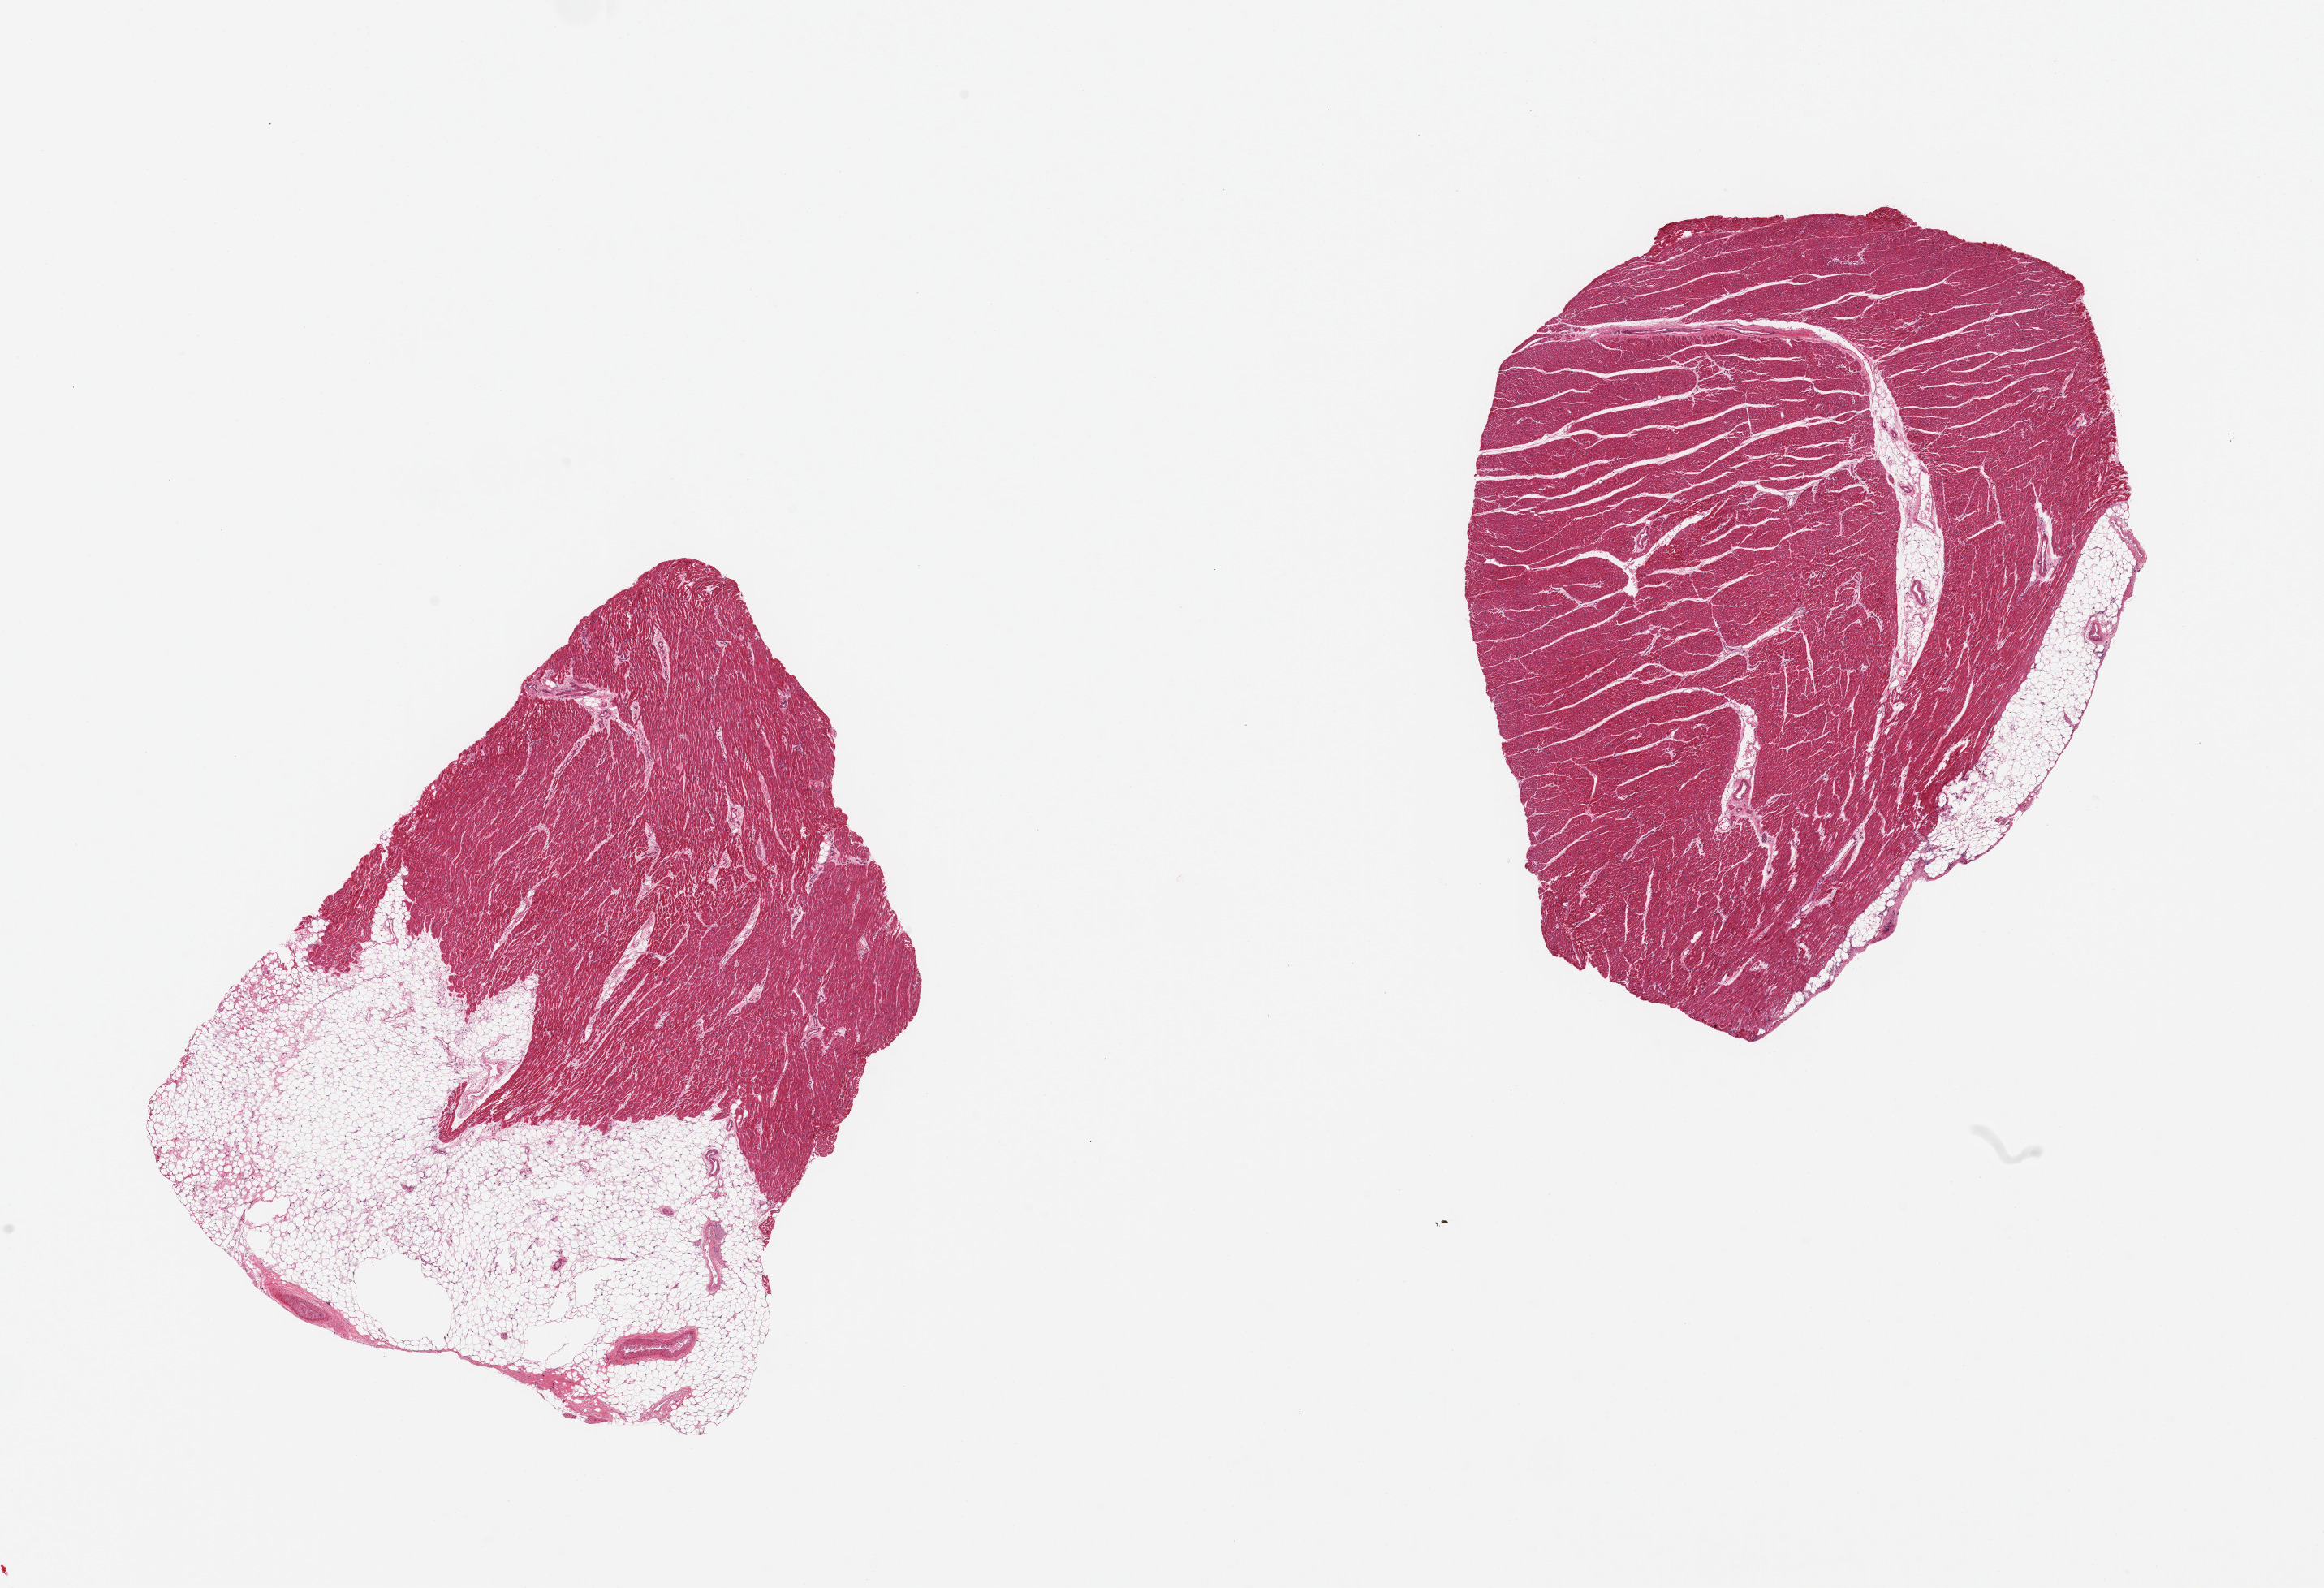
Digitized hematoxylin and eosin (H&E)-stained section, whole scanned area (about 22.6 x 15.5 mm, acquisition: 20x scan) shown as a low-resolution overview; PAXgene-fixed, paraffin-embedded tissue; target tissue: heart; tissue donor sample. Donor sex: female.
Review note (as recorded): 2 pieces; excessive 50% (up to 3 mm) external fat on 1 piece, 10% on other.